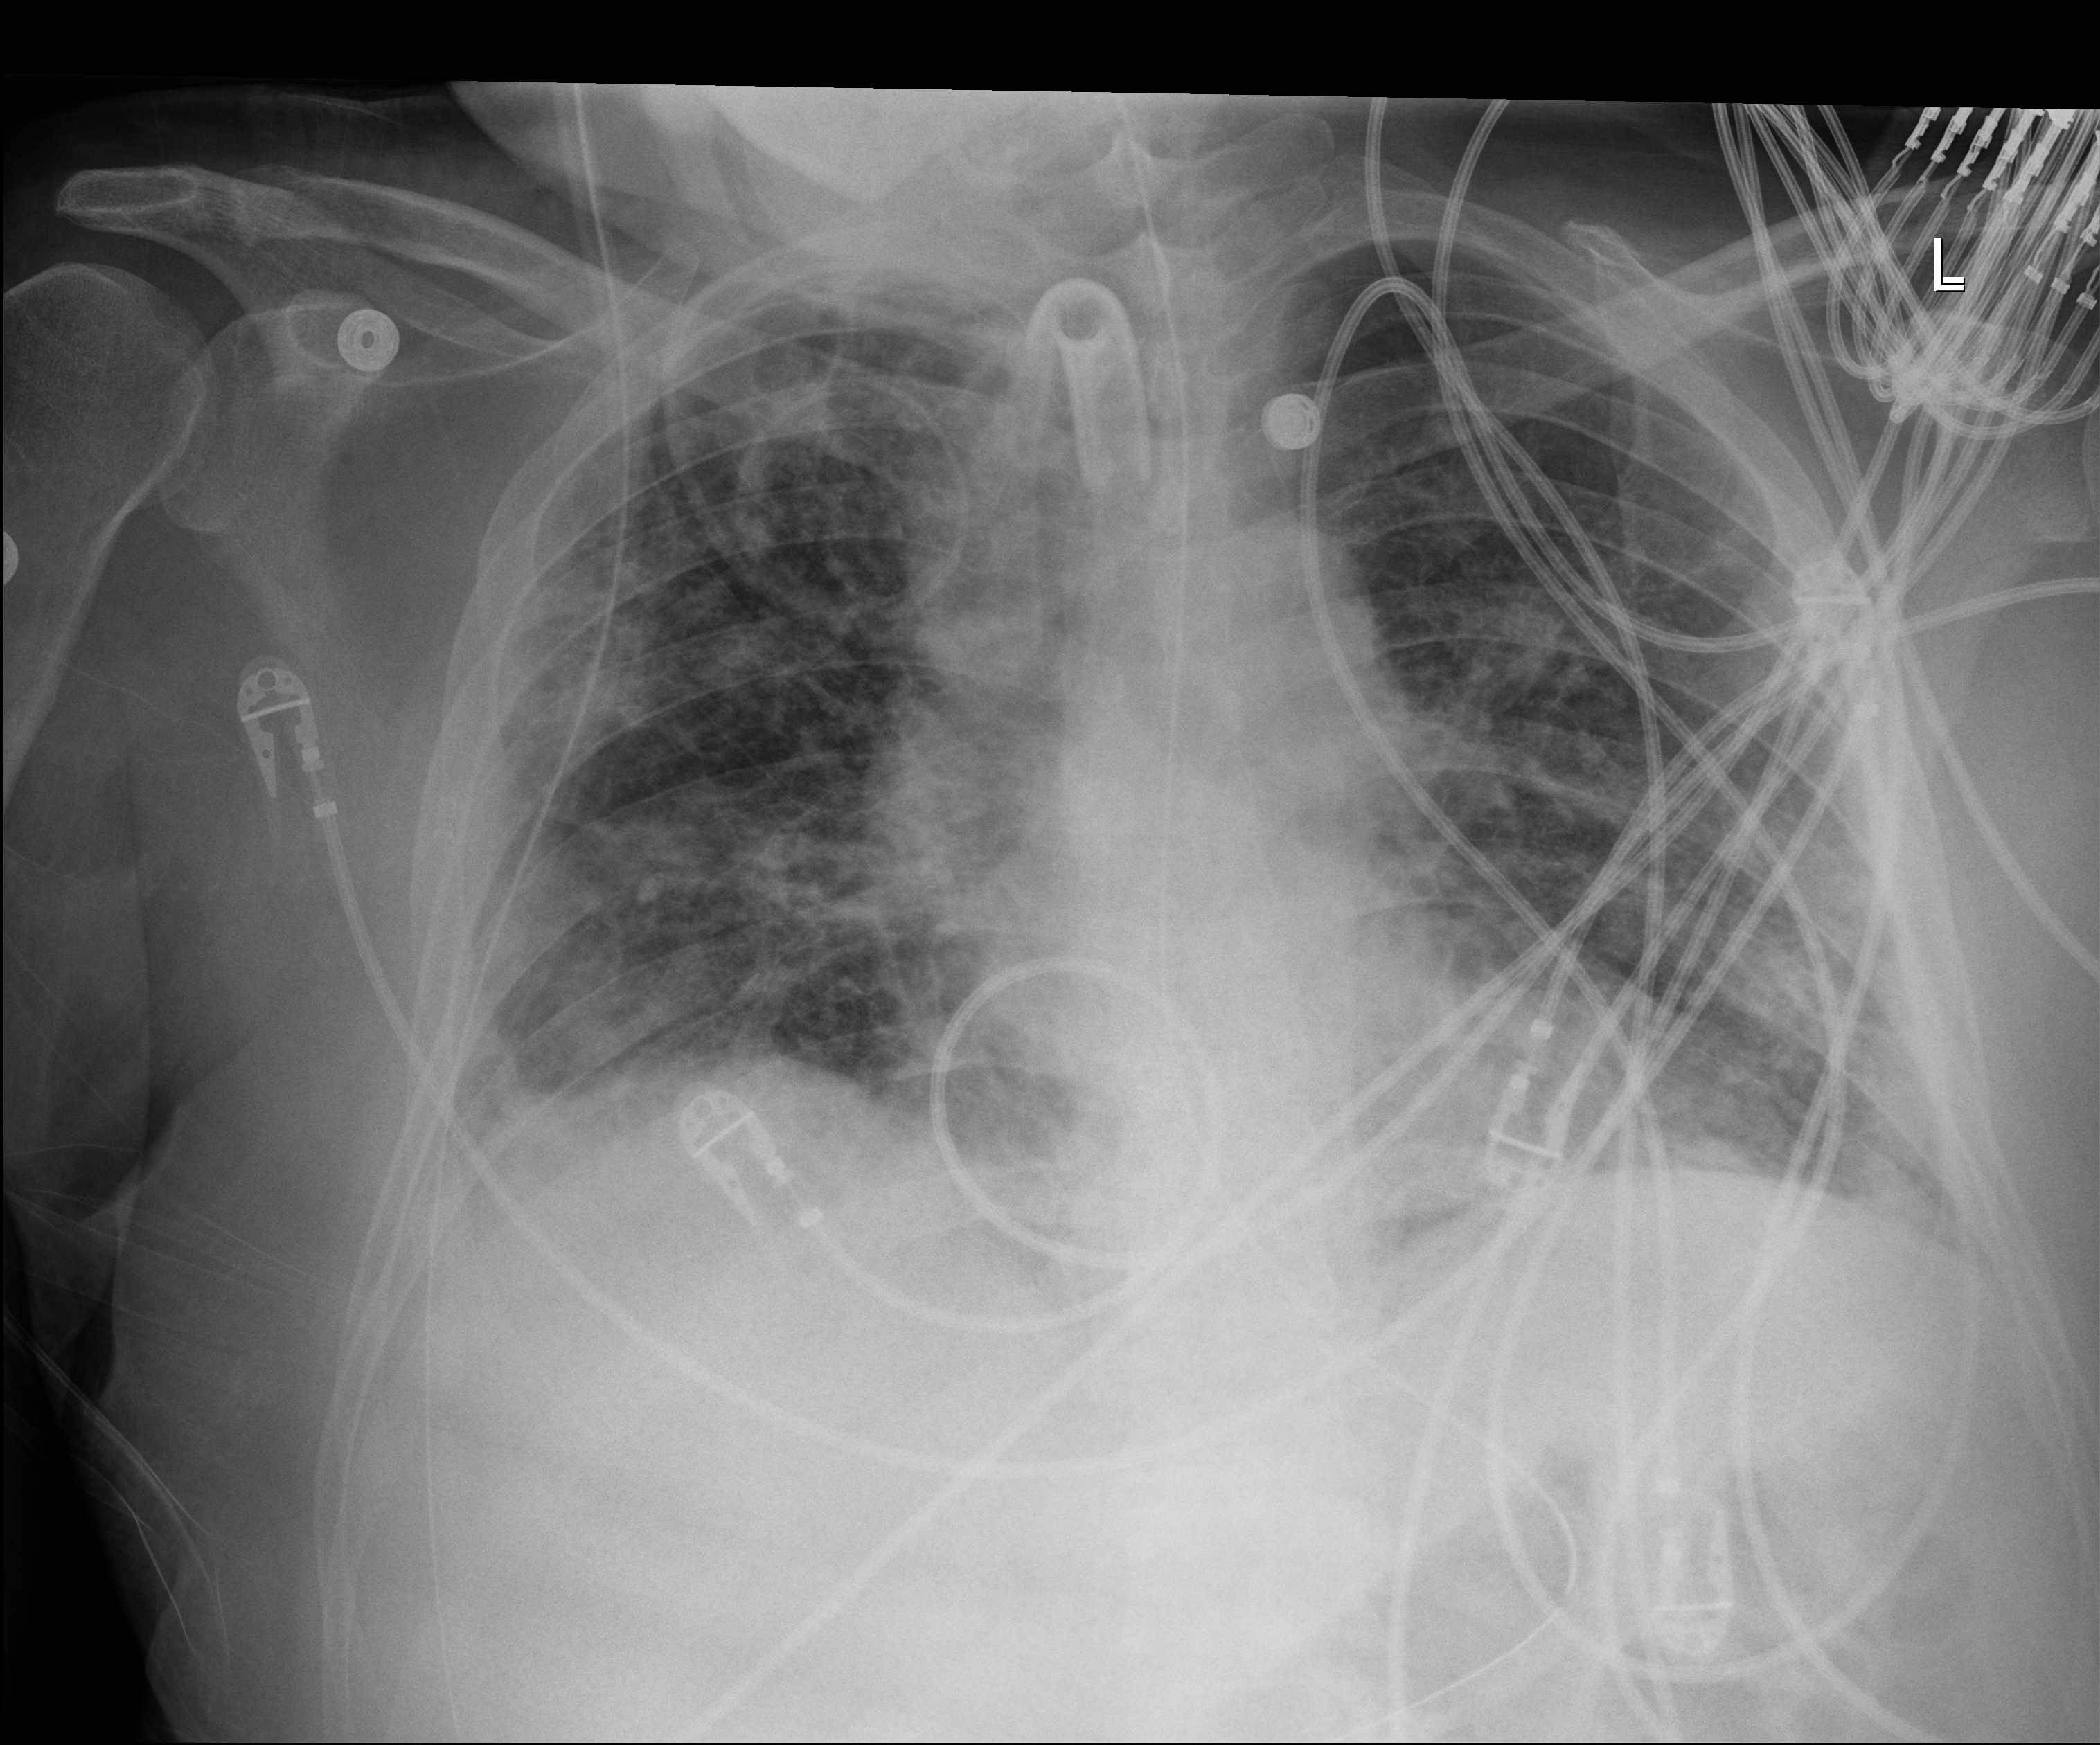
Portable chest radiograph, anteroposterior (AP) projection. Male patient hospitalised with COVID-19, age 18–59 years.
Admission-level facts for this patient (not findings on this image; timing relative to this image not recorded): hypertension (admission record): yes; admitted to intensive care during this hospital stay: yes; other chronic lung disease (admission record): no.